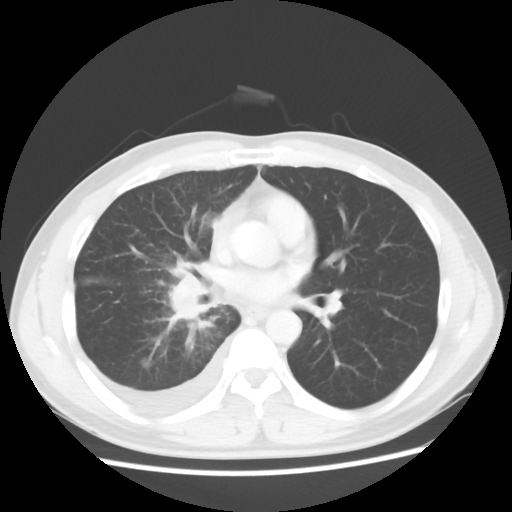
Chest CT, one axial slice. Position 28 of 56 along the scan axis. 120 kVp. Lung window (W 1500 / L -600 HU). 512 × 512 image matrix, field of view 360 × 360 mm. Male patient, age 46 years. Case-level facts recorded for this patient, not image findings: clinical TNM (as recorded): T2 N3 M1.
Annotated regions visible in this slice (bounding box drawn by a radiologist):
- lung tumour (recorded histology: adenocarcinoma): bounding box (x1, y1, x2, y2) in pixels: (163, 271, 207, 331)